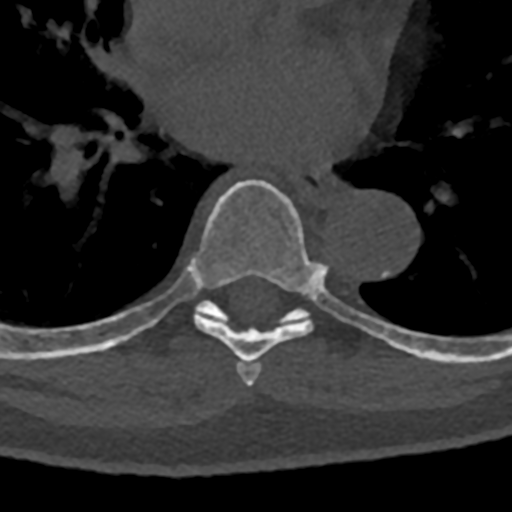
CT including the spine, one axial slice; slice 750 of 797 in the series (ordered by position); reconstruction kernel Br40s/3; 120 kVp; bone window (W 1800 / L 400 HU); 512 × 512 image matrix. Patient: male, 74 years. From the clinical record (not read from this slice): primary cancer: renal; vertebrae with lytic lesions (as recorded): T10, L1, L2, L3, L4, L5.
Outlined on this slice (semi-automatic segmentation, software-assisted and operator-edited):
- T6 vertebra: bounding box [x1, y1, x2, y2] px = [236, 362, 262, 386]
- T7 vertebra: [71, 179, 378, 364]
- T8 vertebra: [70, 301, 432, 360]